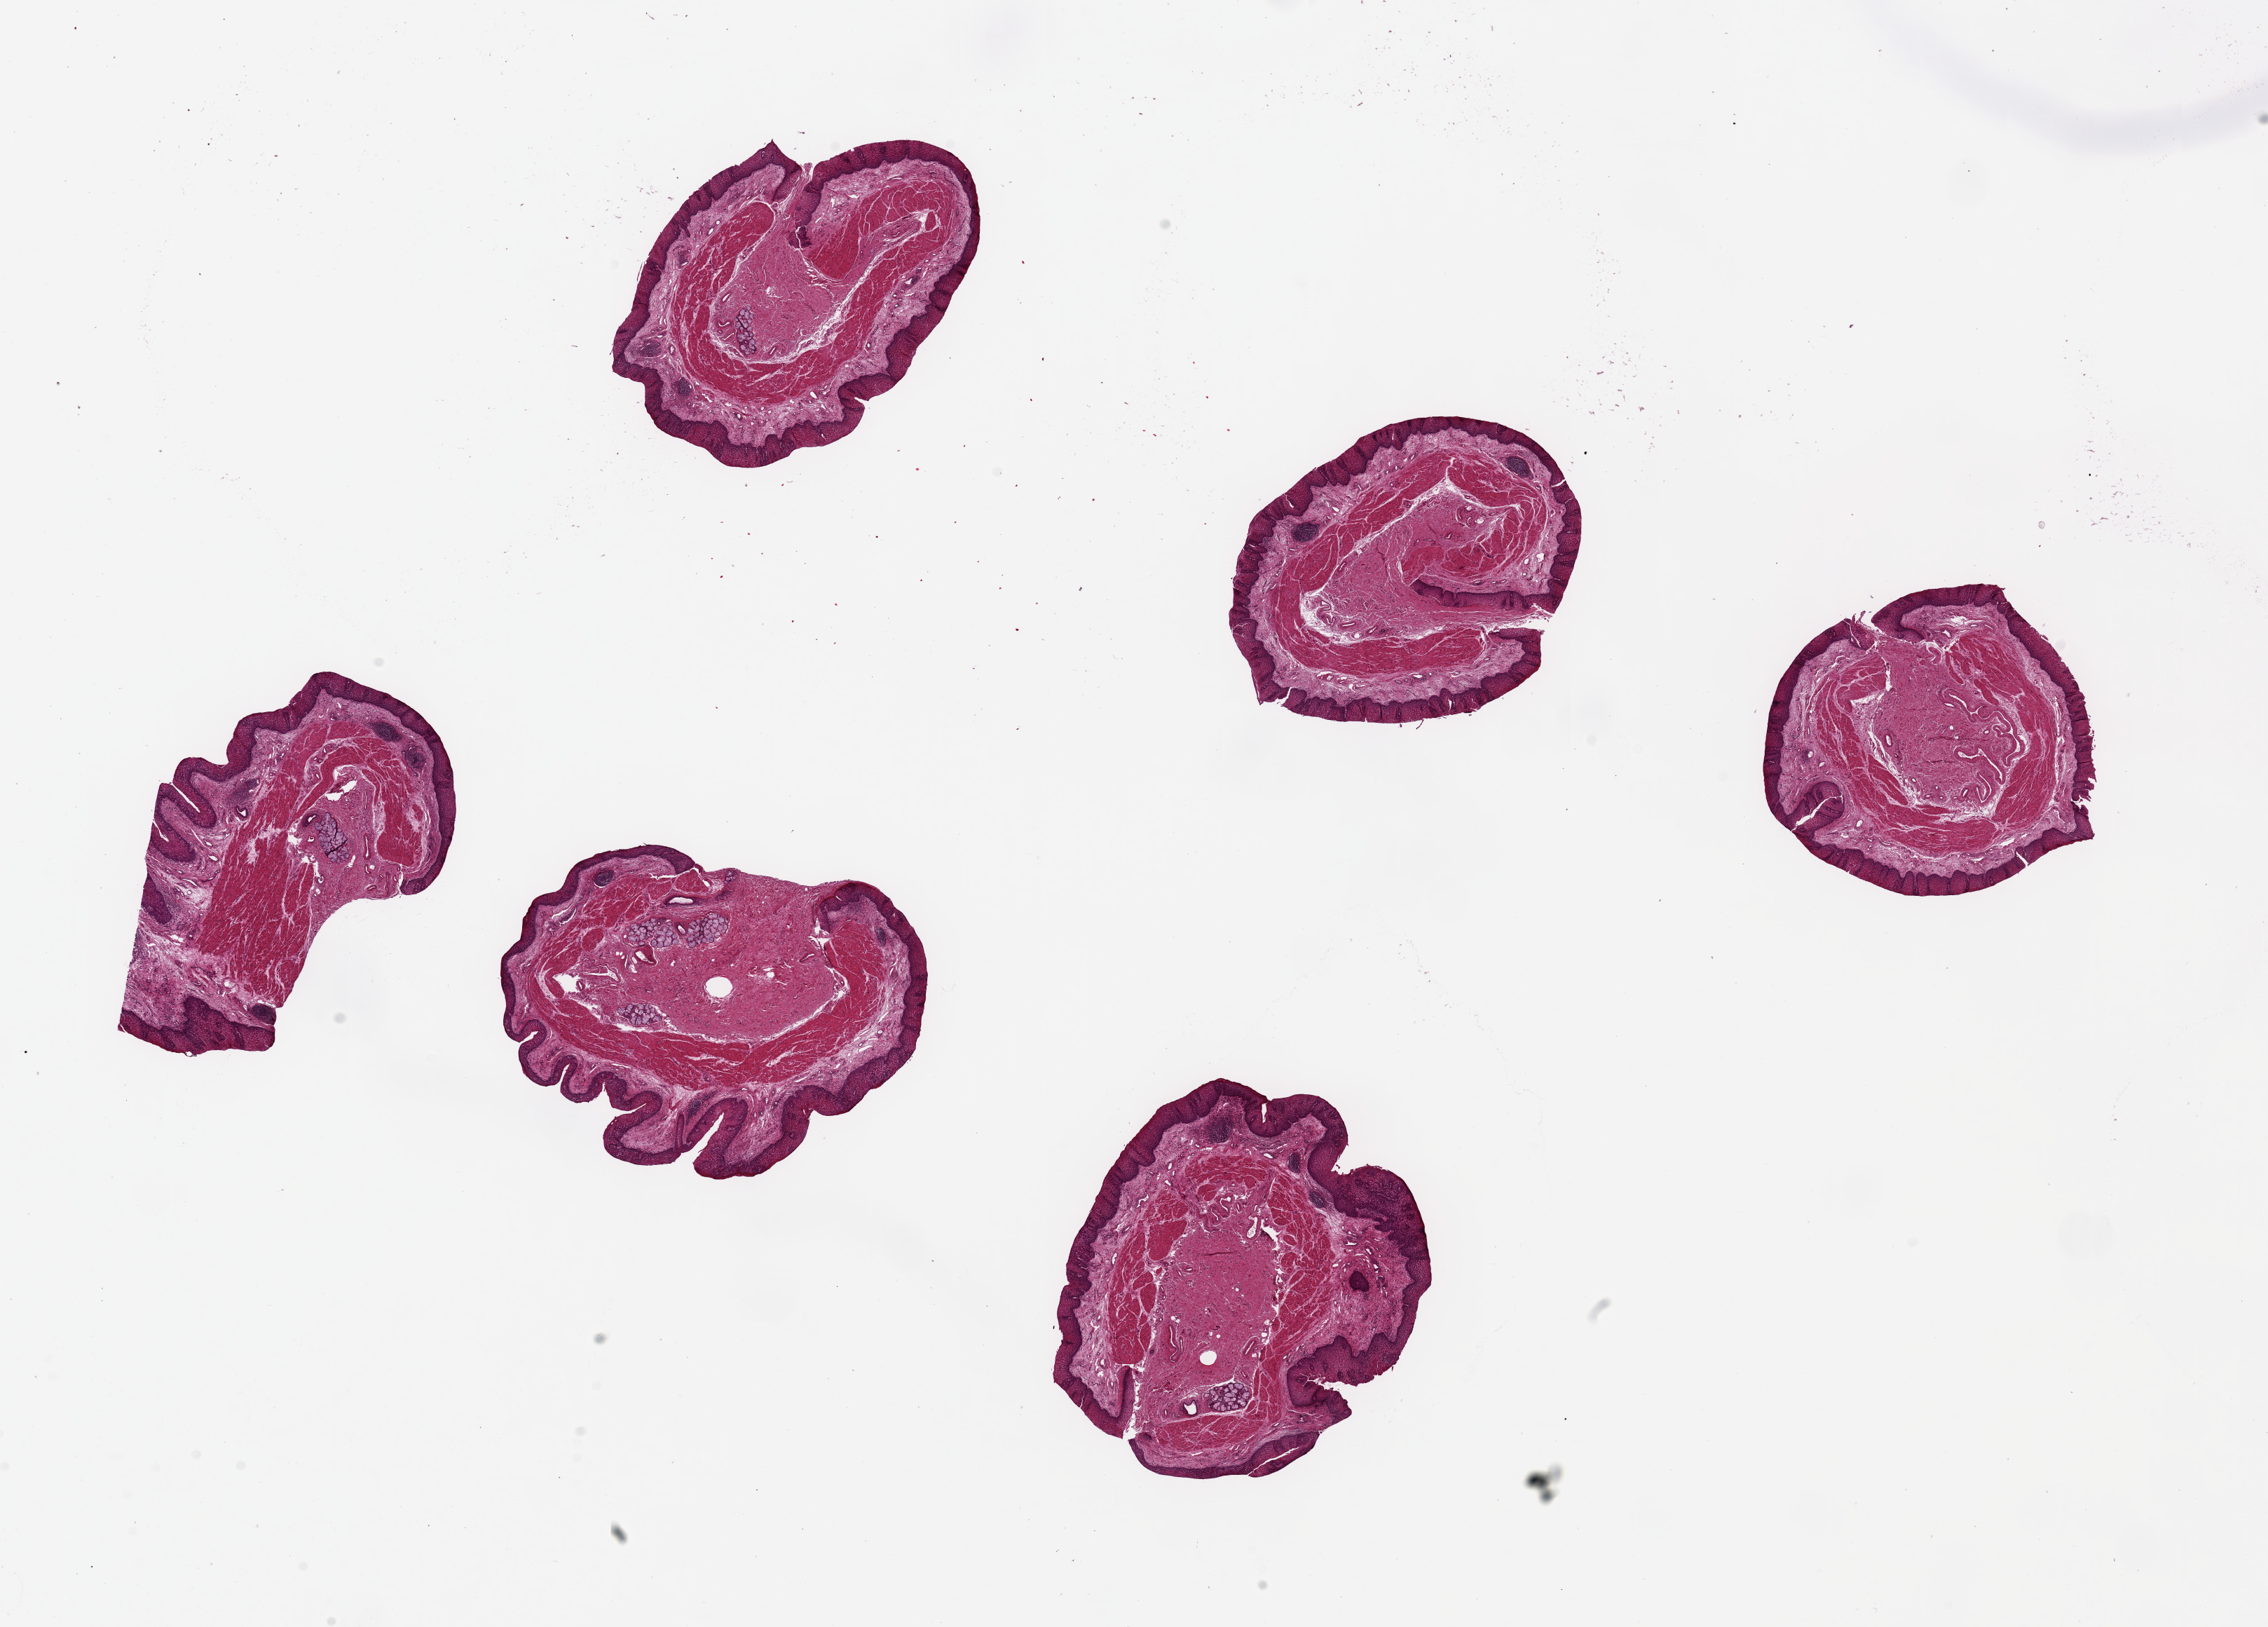
Digitized H&E-stained section, brightfield, whole scanned area (about 25.6 x 18.4 mm) shown as a low-resolution overview; PAXgene-fixed, paraffin-embedded tissue; sampled site (target tissue): esophageal mucous membrane; tissue donor sample.
Review note (as recorded): 6 pieces, up to 4.5x4mm; squamous mucosa is ~10-20% thickness.